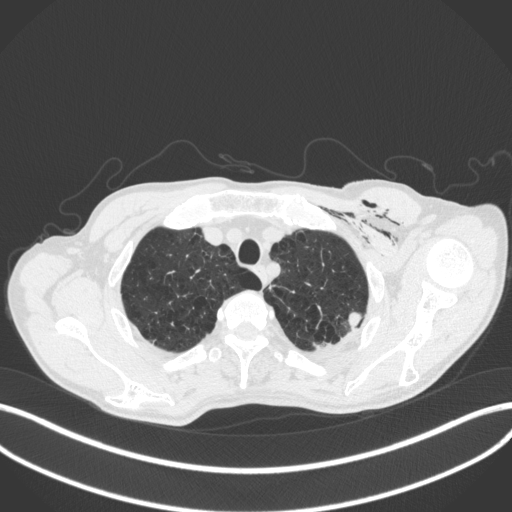
Chest CT, one axial slice. Slice 357 of 416 in the series (ordered by position). Reconstruction kernel B31f. Lung window (W 1500 / L -600 HU). 1 mm slice thickness. 512 × 512 image matrix. Patient: male, 58 years. From the clinical record (not read from this slice): clinical TNM (as recorded): T3 N0 M0.
Outlined on this slice (bounding box drawn by a radiologist):
- lung tumour (recorded histology: adenocarcinoma): box from (x=346, y=312) to (x=367, y=331) px